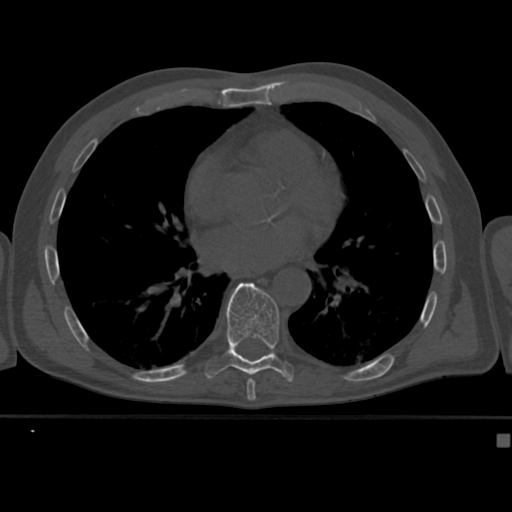
CT including the spine, one axial slice; position 248 of 430 along the scan axis; bone window (W 1800 / L 400 HU); 1.5 mm slice thickness; 512 × 512 image matrix. Male patient, age 64 years. Case-level facts recorded for this patient, not image findings: primary cancer: uterus.
Annotated regions visible in this slice (semi-automatically segmented with operator editing):
- T8 vertebra: box from (x=247, y=378) to (x=254, y=382) px
- T9 vertebra: (x=204, y=282)–(x=295, y=382)